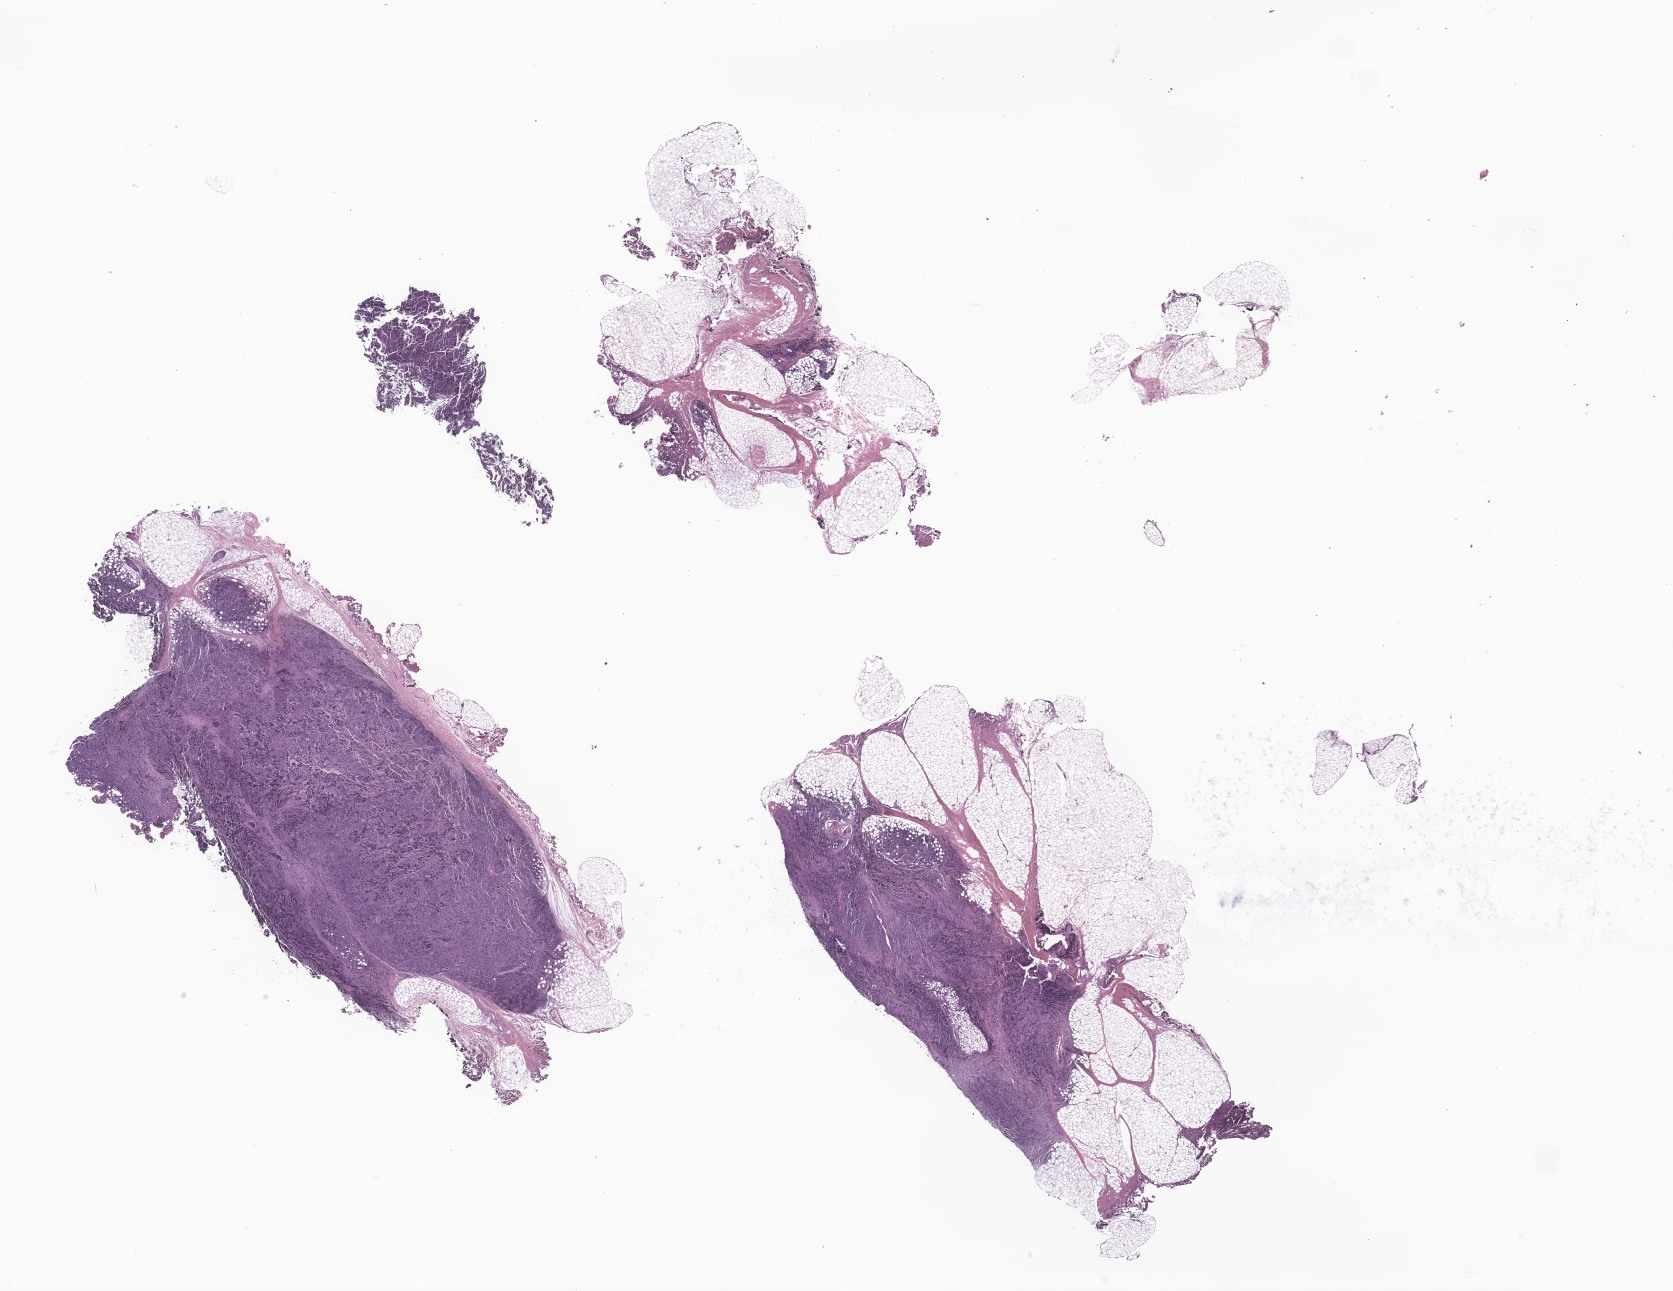
Digitized H&E-stained section of tumor tissue from the abdomen, low-resolution overview of the scanned area, about 28.2 x 21.8 mm; formalin-fixed, paraffin-embedded (FFPE) tissue. Patient male; age 203 days.
Recorded diagnosis: Neuroblastoma, NOS.